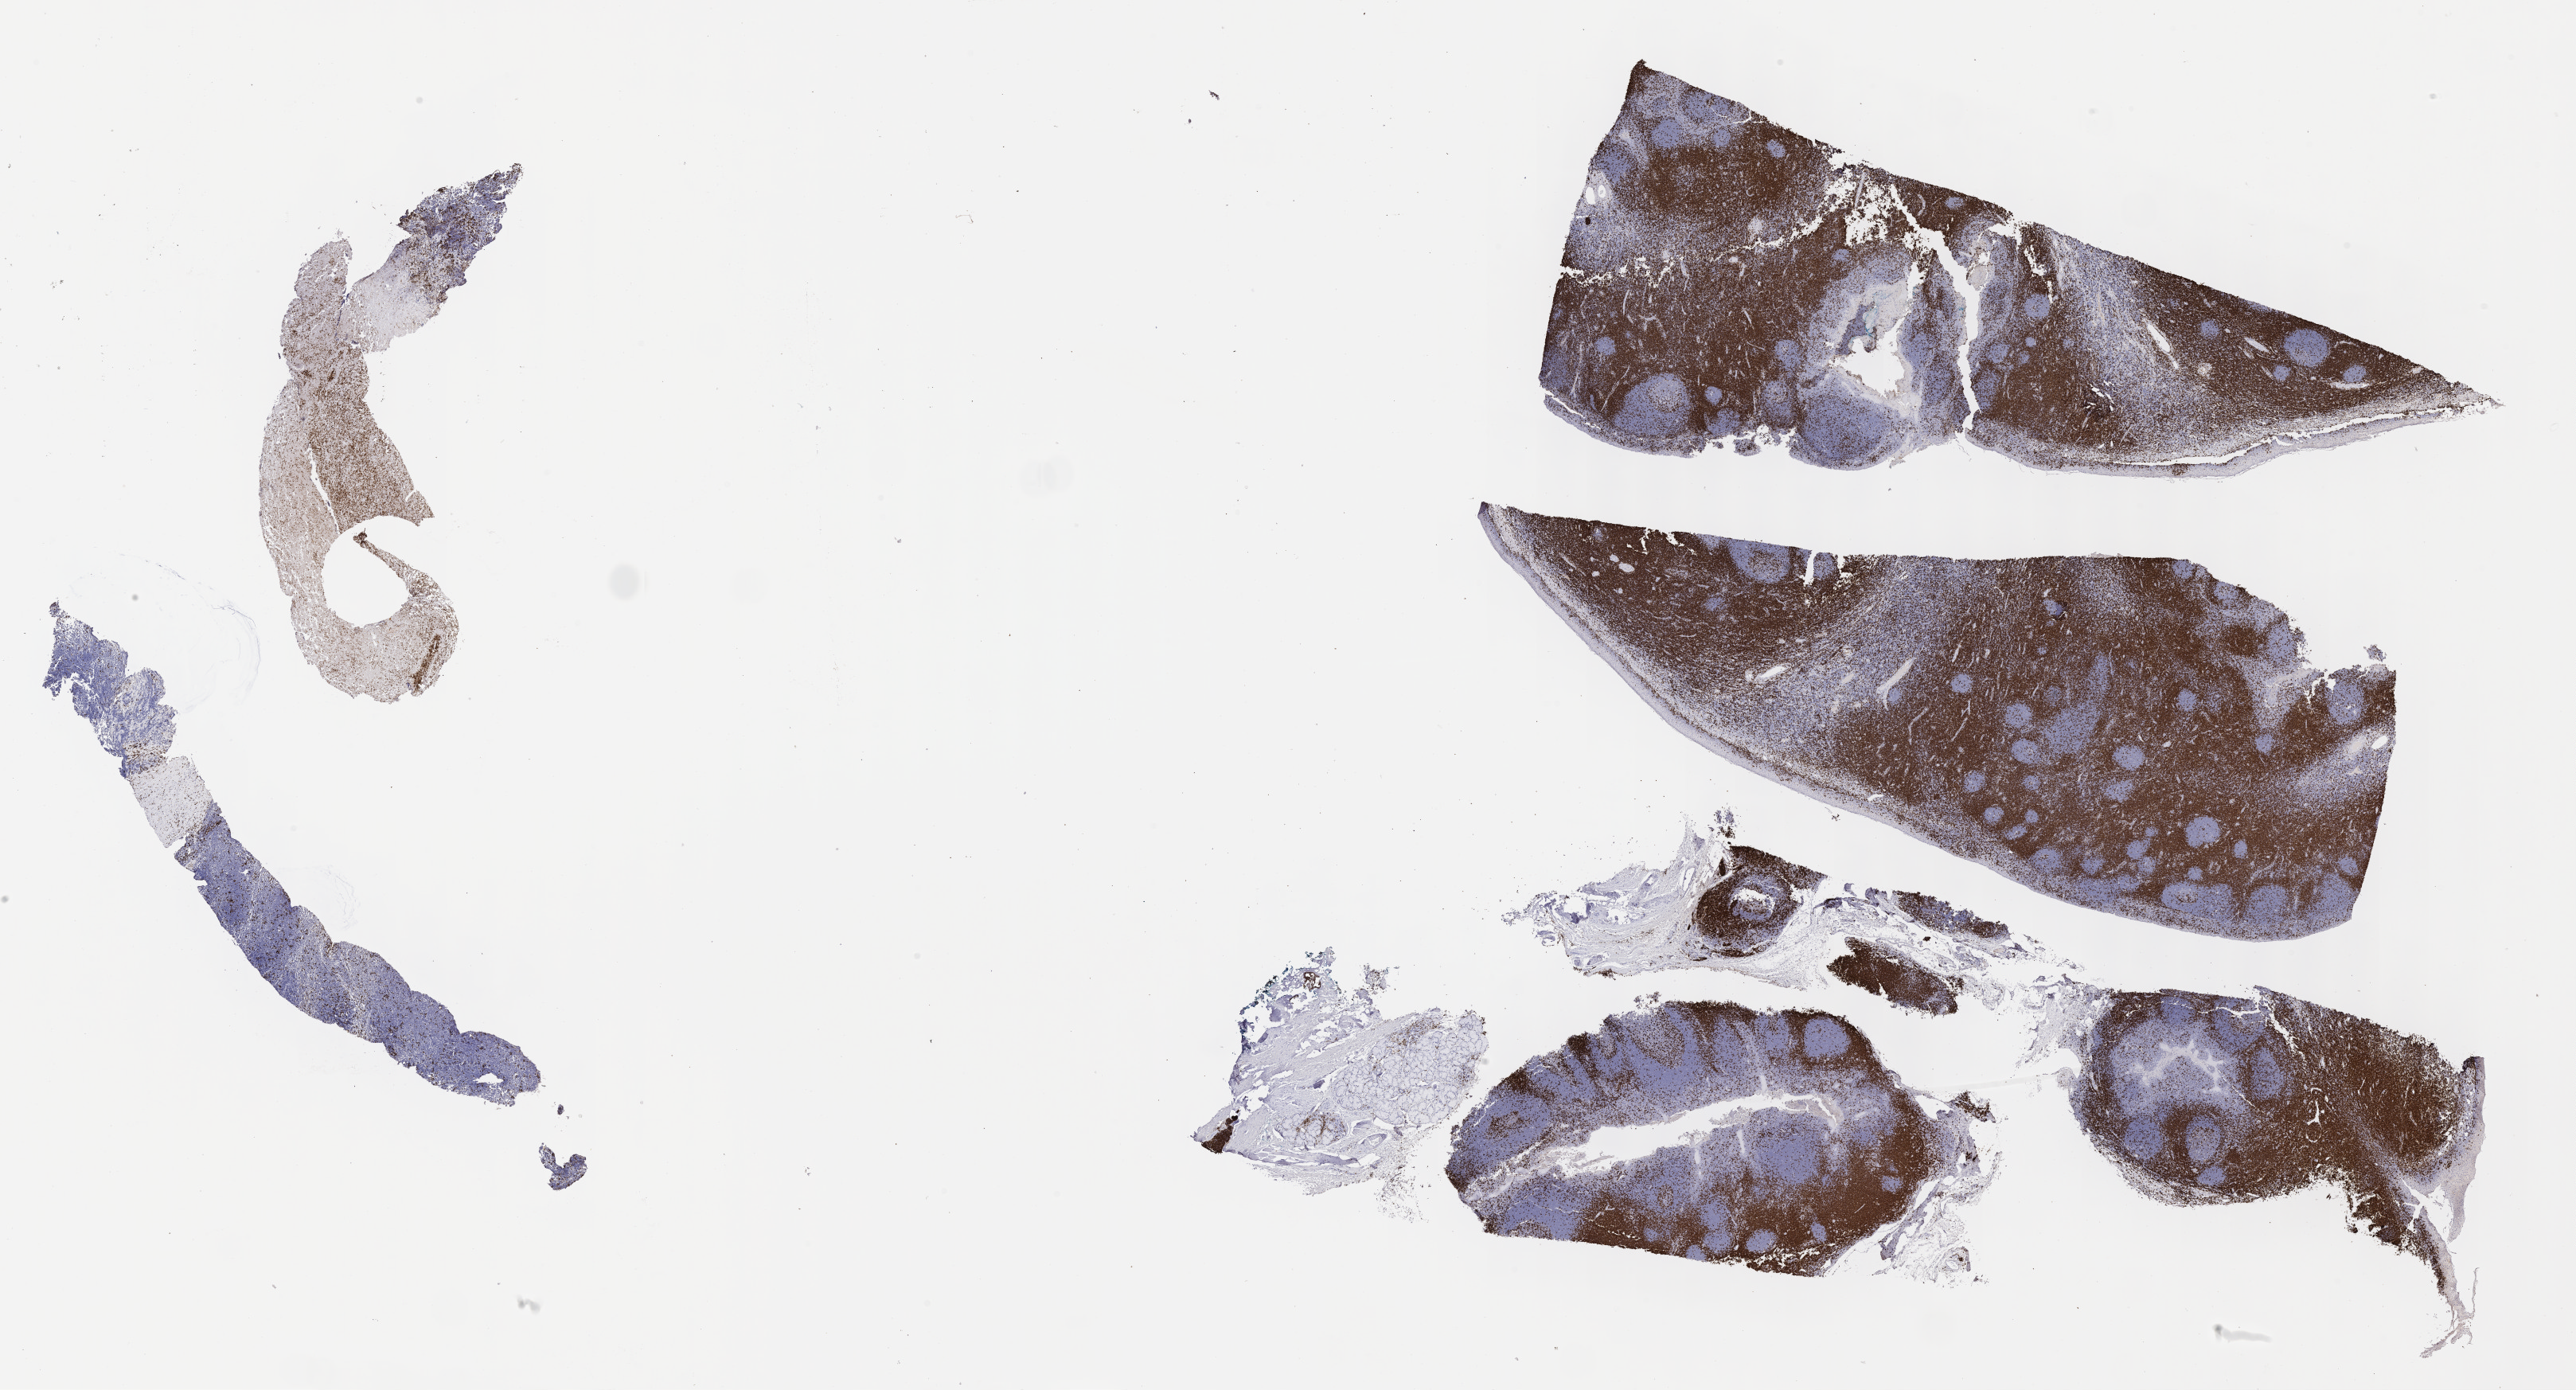
Immunohistochemistry (IHC) whole-slide image stained for CD3, whole scanned area (about 26.2 x 14.1 mm) shown as a low-resolution overview, tumor tissue. Patient male; aged 10.
Histologic diagnosis: Burkitt lymphoma, NOS.